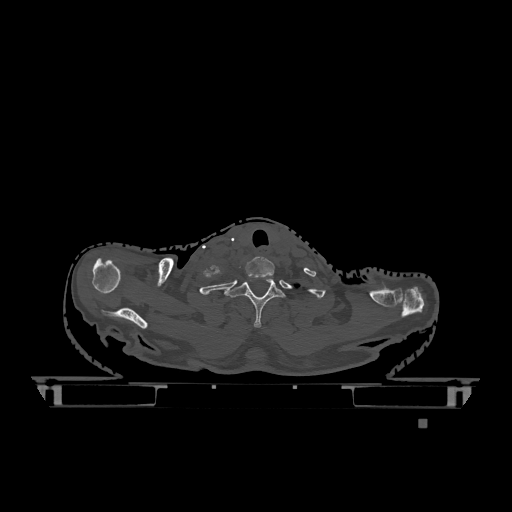
CT including the spine, one axial slice; slice 1004 of 1317 in the series (ordered by position); bone window (W 1800 / L 400 HU); 0.5 mm slice thickness; 512 × 512 image matrix. Female patient, age 74 years. Case-level facts recorded for this patient, not image findings: primary cancer: lung; vertebrae with lytic lesions (as recorded): T1, T4, T5, T6, L4, L5.
Annotated regions visible in this slice (semi-automatically segmented with operator editing):
- T1 vertebra: box from (x=225, y=276) to (x=285, y=328) px